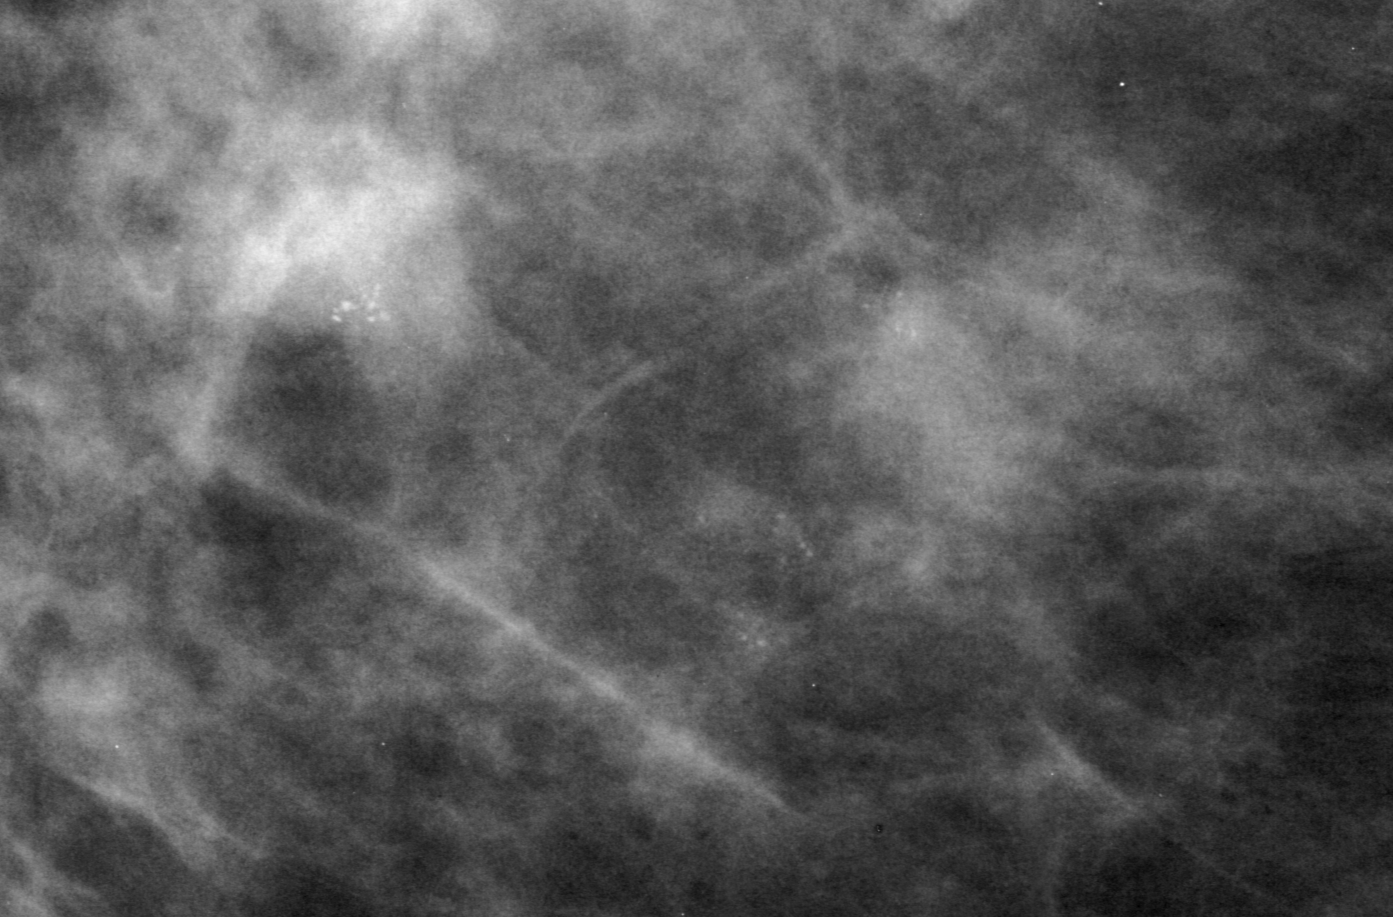
Crop from a digitized film mammogram around one marked abnormality; right breast; CC view; BI-RADS breast density category 2 (scale 1–4).
Finding: calcifications, morphology pleomorphic, distribution clustered; BI-RADS assessment category 0; pathology result (as recorded, not read from the image): malignant.